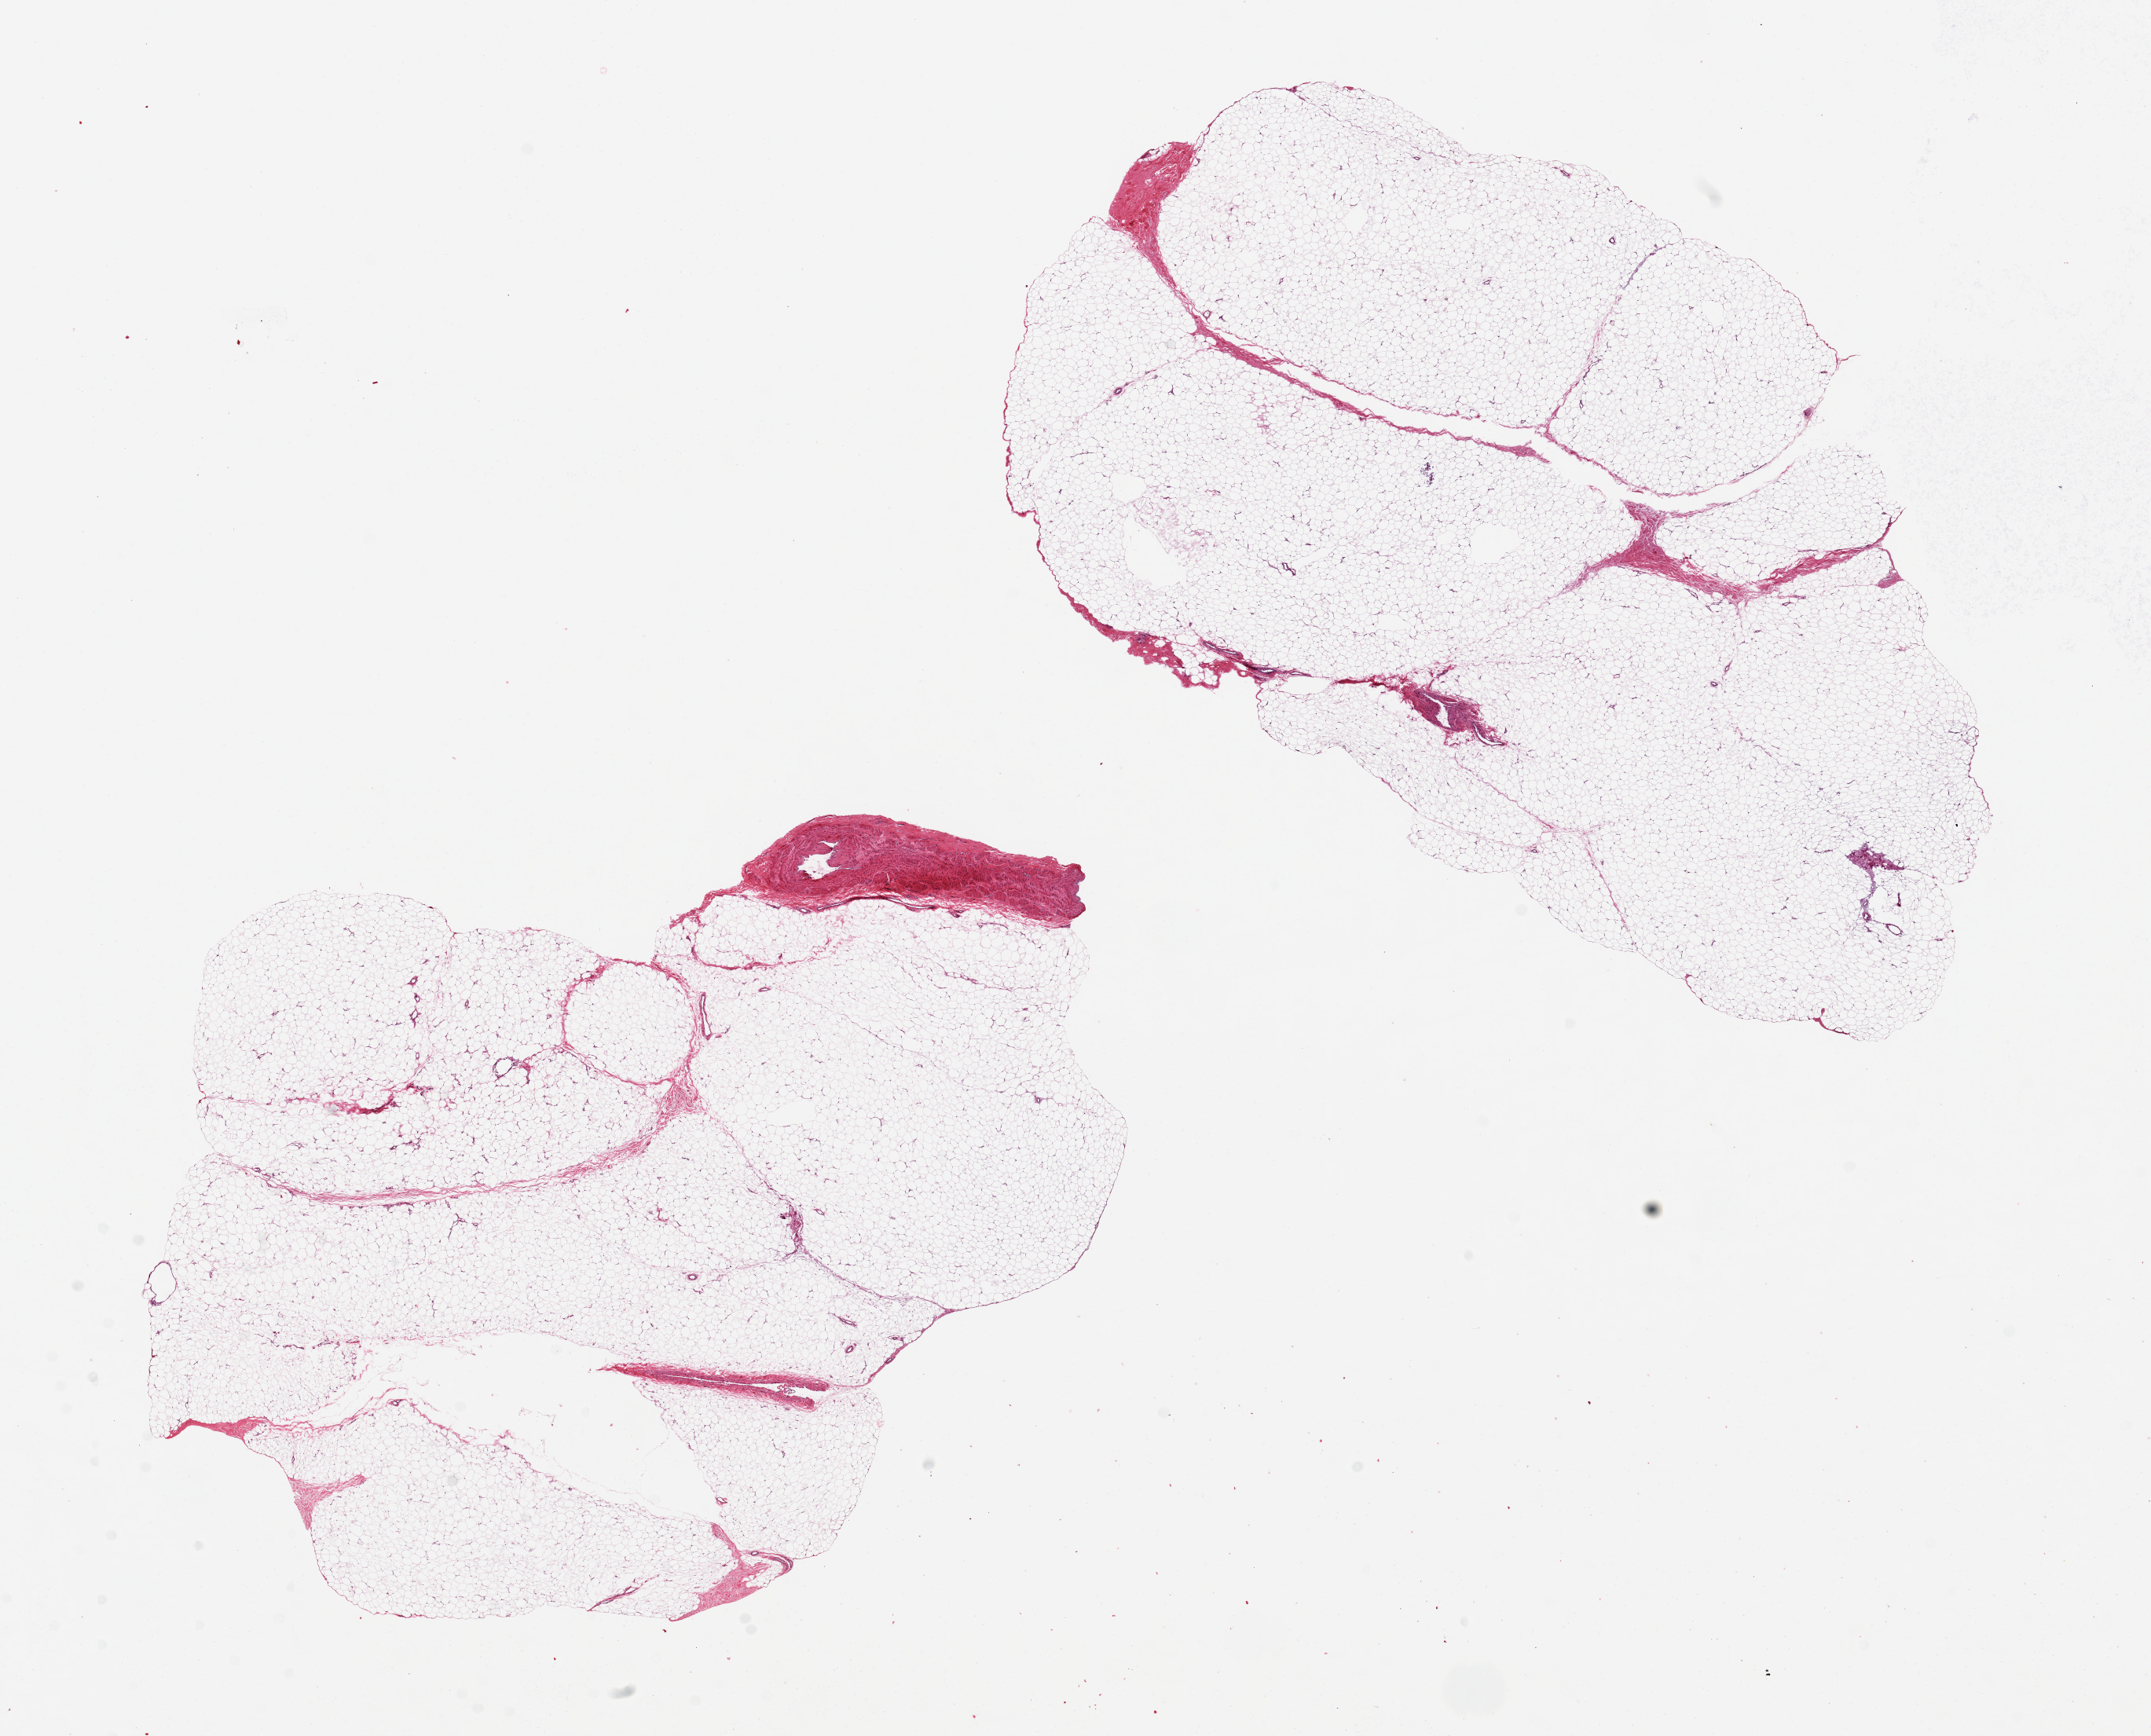
Whole-slide image, hematoxylin and eosin (H&E) stain — a low-resolution overview of the entire scanned area, about 21.7 x 17.5 mm, PAXgene-fixed paraffin-embedded (PFPE) section, target tissue: adipose tissue, donor tissue sample. Male donor.
Reviewer comment on this tissue sample: 2 pieces, 10.5x8 & 11.5x7 mm. No fixation artifacts. Adherent vessel, 1 x 3 mm.